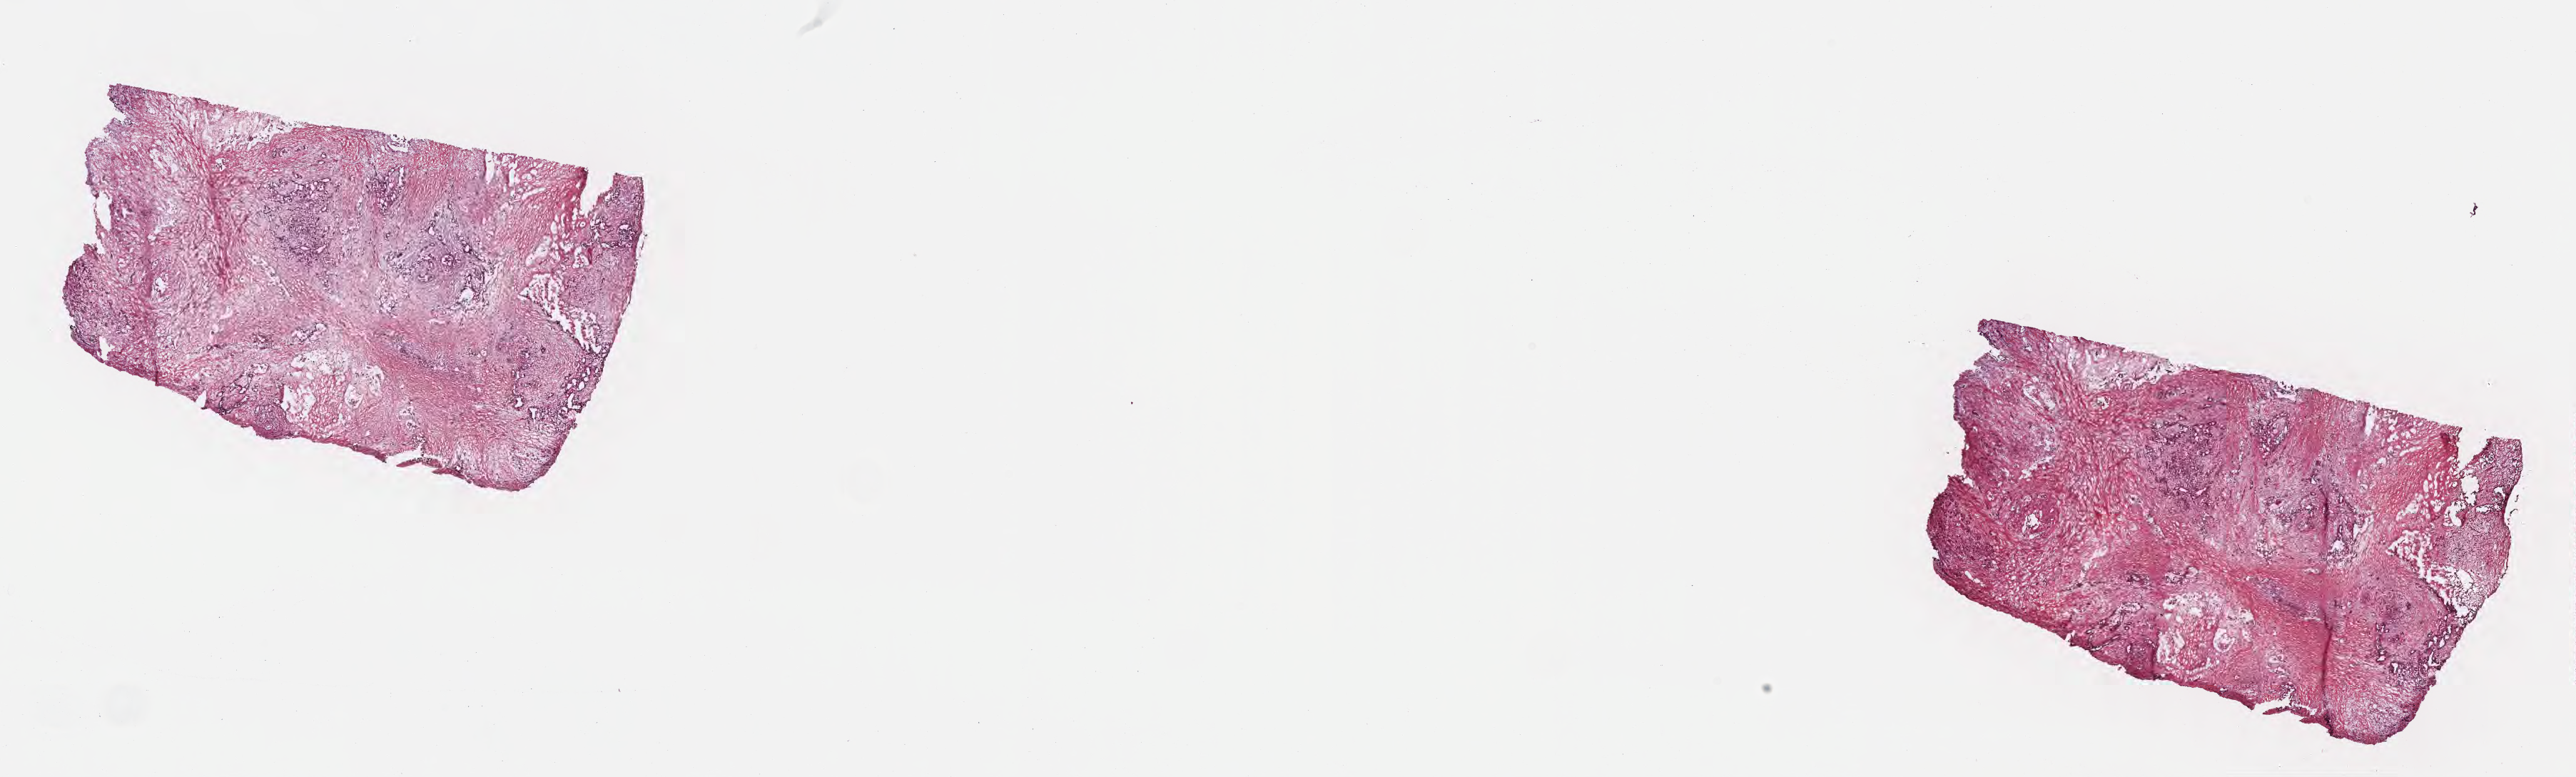
Haematoxylin and eosin whole-slide image, low-resolution overview of the scanned area, about 29.2 x 8.8 mm. Cryosection. Primary tumor. Site: body of pancreas. Female patient; age at initial diagnosis 74 years. Tumor grade: G2 (moderately differentiated). Pathologist review of this section (percent, as recorded): tumor cells 40%, tumor nuclei 40%, stromal cells 20%, necrosis 5%, normal cells 35%. Inflammatory infiltration, as recorded: lymphocyte infiltration 7%, monocyte infiltration 1%, neutrophil infiltration 5%.
Diagnosis: Infiltrating duct carcinoma, NOS. AJCC pathologic stage: Stage IIB.